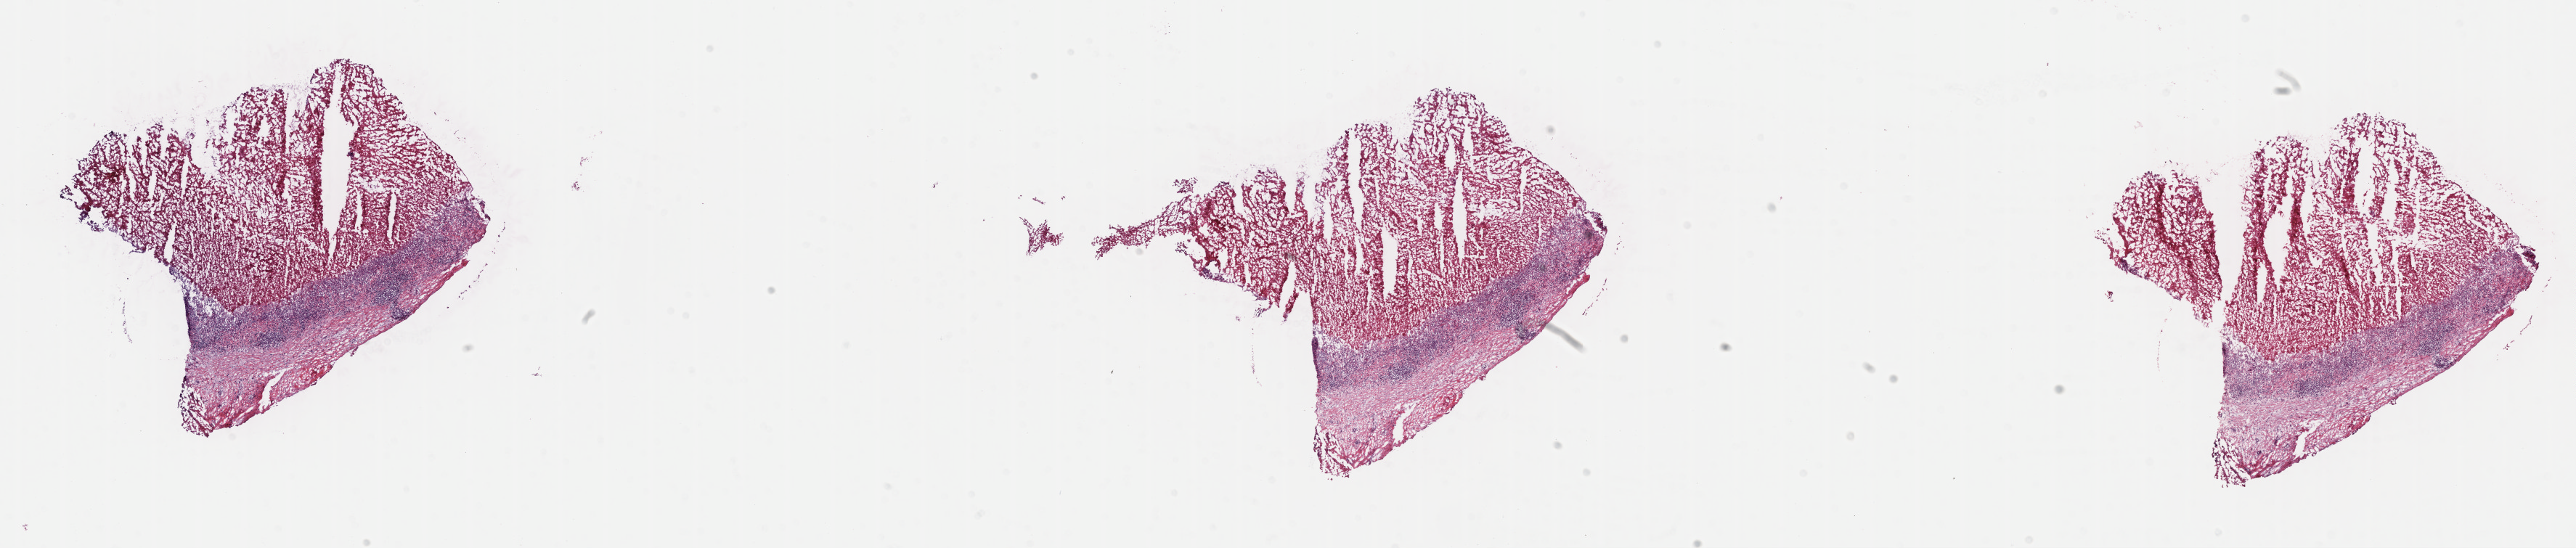
Digitized haematoxylin and eosin-stained section — shown as a low-resolution overview of the whole scanned area (about 28.7 x 6.1 mm), frozen section, primary tumor, site: lymph node of head and neck. Male patient; age at initial diagnosis 5 years. Pathologist review of this section (percent, as recorded): tumor cells 70%, tumor nuclei 90%, stromal cells 20%, necrosis 10%, normal cells 0%. Inflammatory infiltration, as recorded: lymphocyte infiltration 3%, monocyte infiltration 2%, neutrophil infiltration 0%.
* Ann Arbor stage (patient): Stage I
* diagnosis: Burkitt lymphoma, NOS